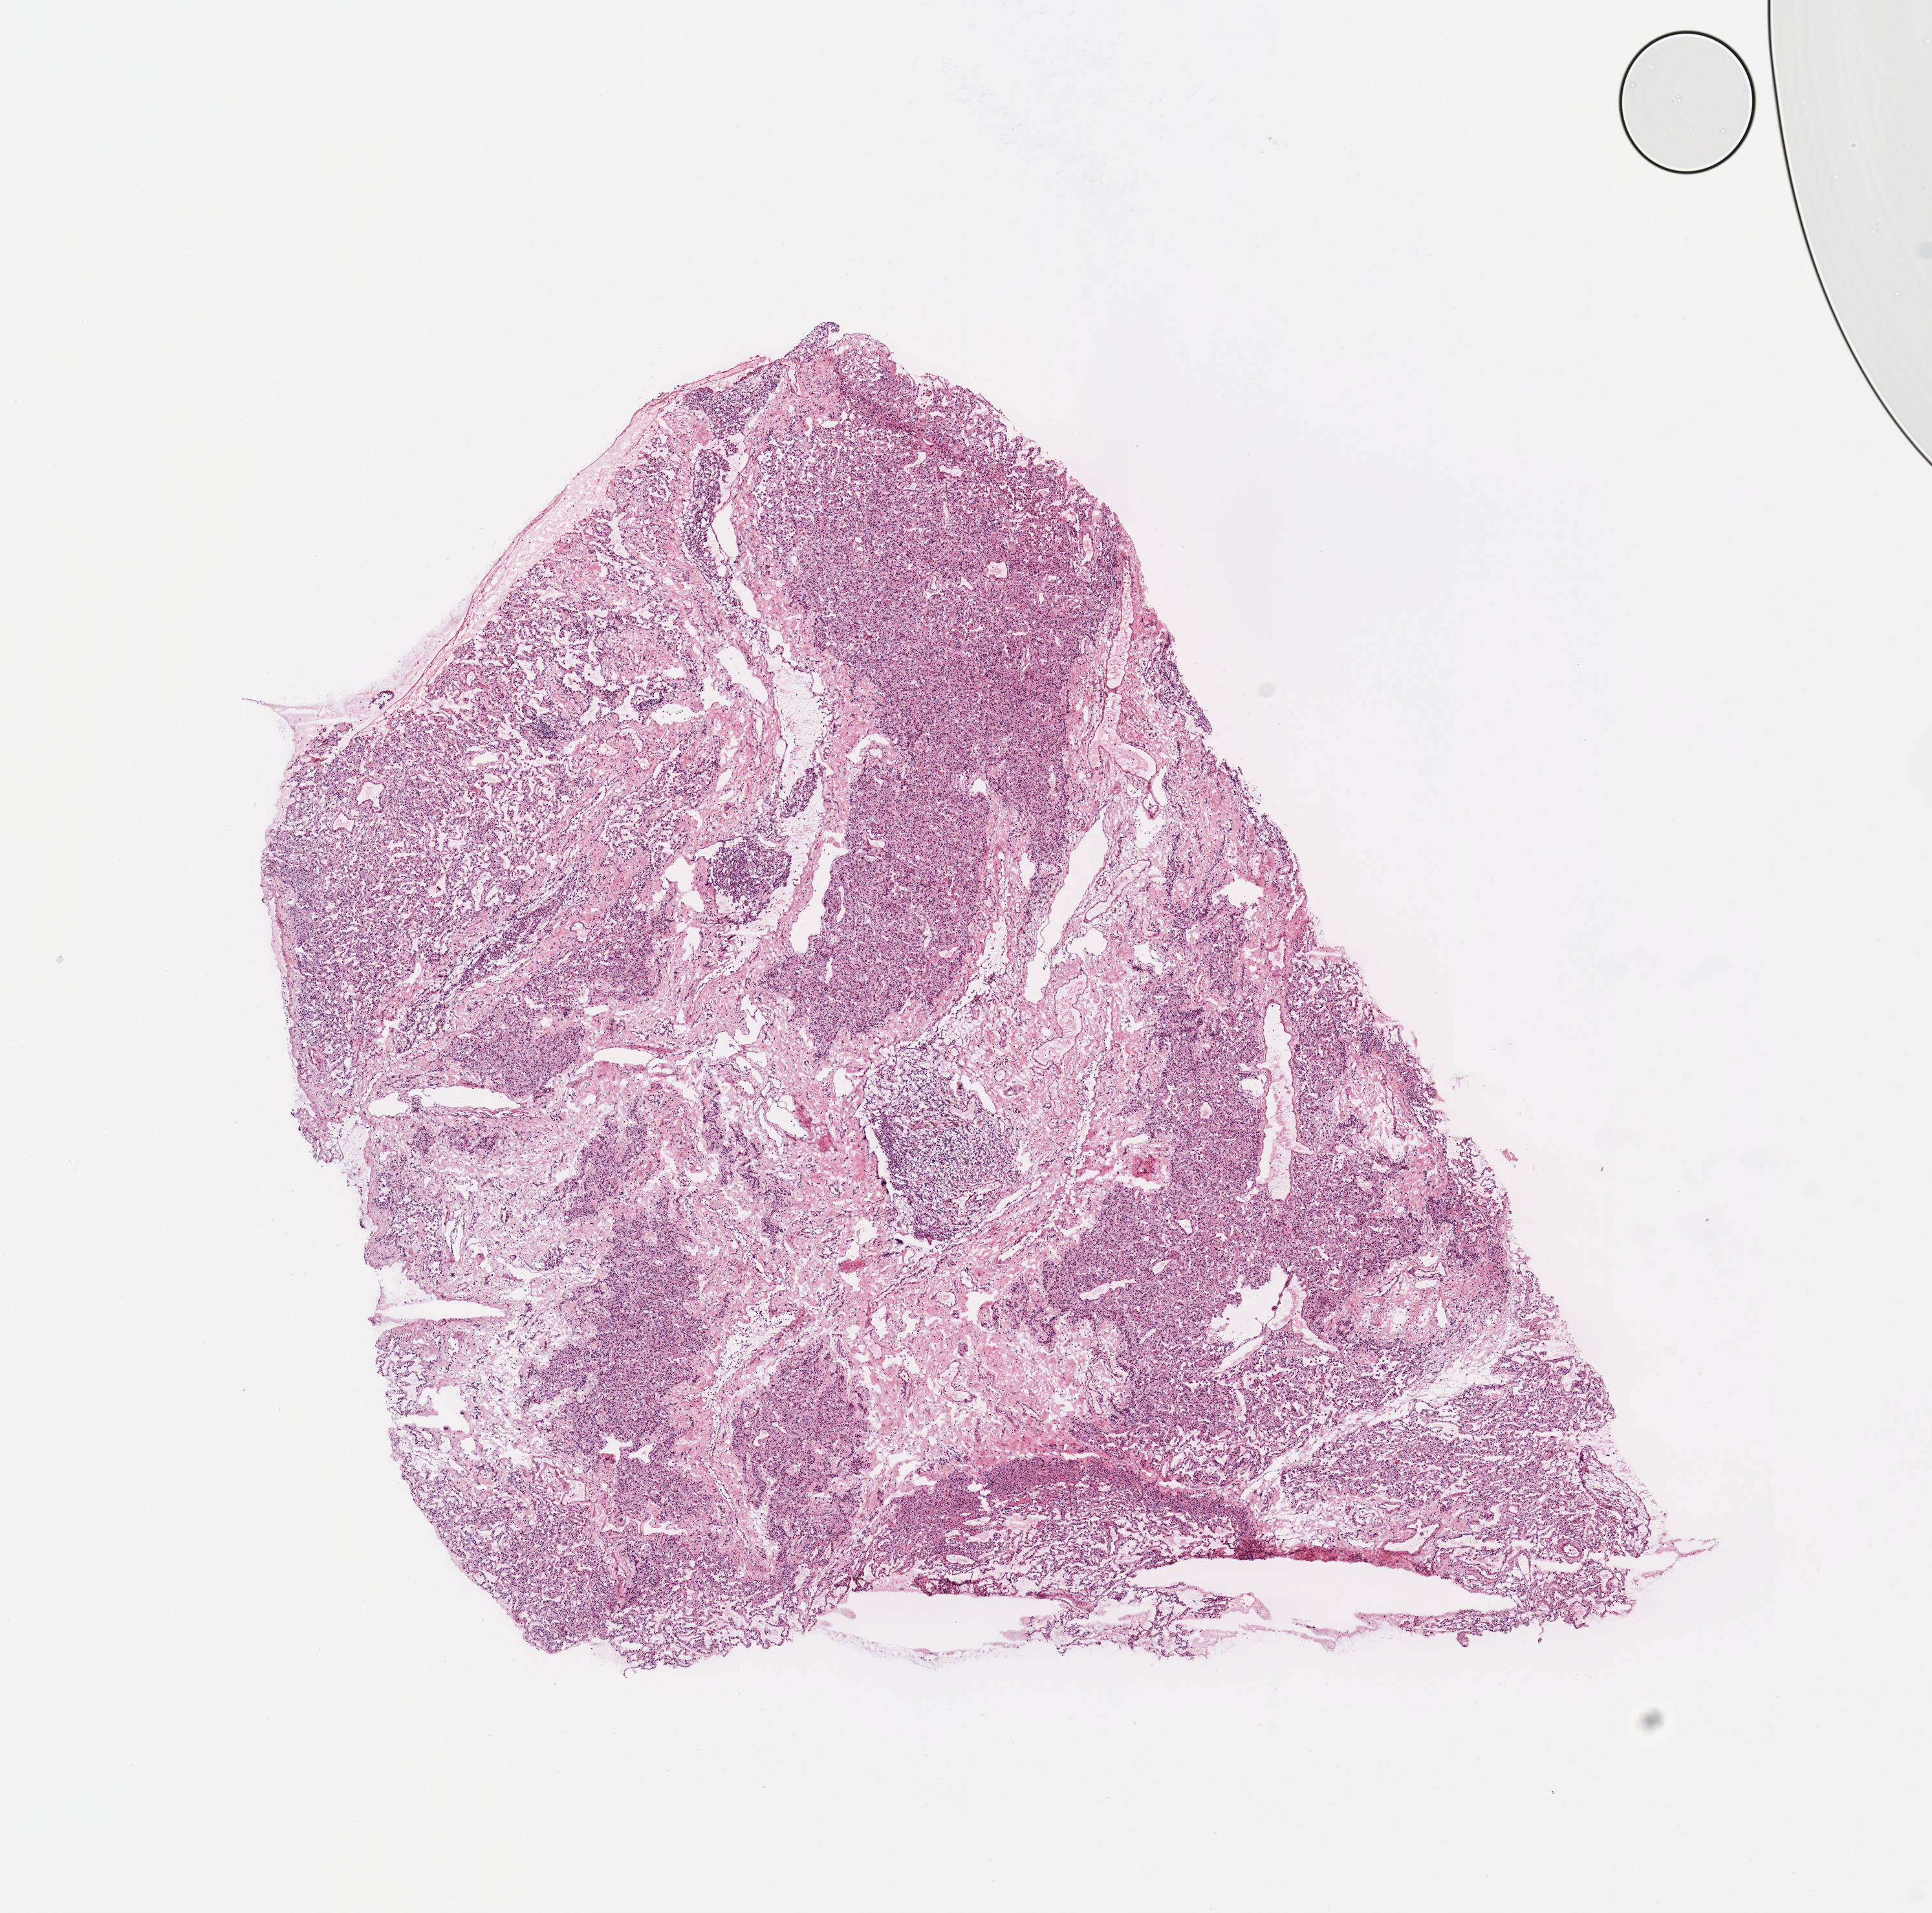
Digitized H&E-stained tissue section (whole slide) — low-resolution overview of the scanned area, about 11.8 x 11.7 mm (acquisition: 20x scan); normal (non-tumour) tissue sample, sampled site: lung. Patient: female, age 35 years.
This section: normal (non-tumour) tissue from the same patient. Patient diagnosis: Adenocarcinoma, NOS.